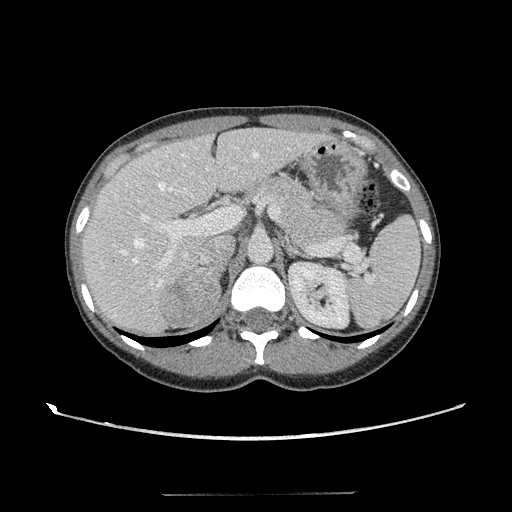
Contrast-enhanced abdominal CT, one axial slice; slice 75 of 117 in the series (ordered by position); 120 kVp; intravenous contrast given; soft-tissue window (W 400 / L 40 HU); 512 × 512 image matrix. Female patient, age 35 years. Case-level facts recorded for this patient, not image findings: diagnosis: adrenocortical carcinoma; tumour side: right adrenal; tumour size at pathology: 3 cm; Ki-67 index: 21 %; stage (as recorded): 3.
Outlined on this slice (semi-automatic segmentation, software-assisted and operator-edited):
- mass: bounding box <161,273,221,325> (left, top, right, bottom; pixels)